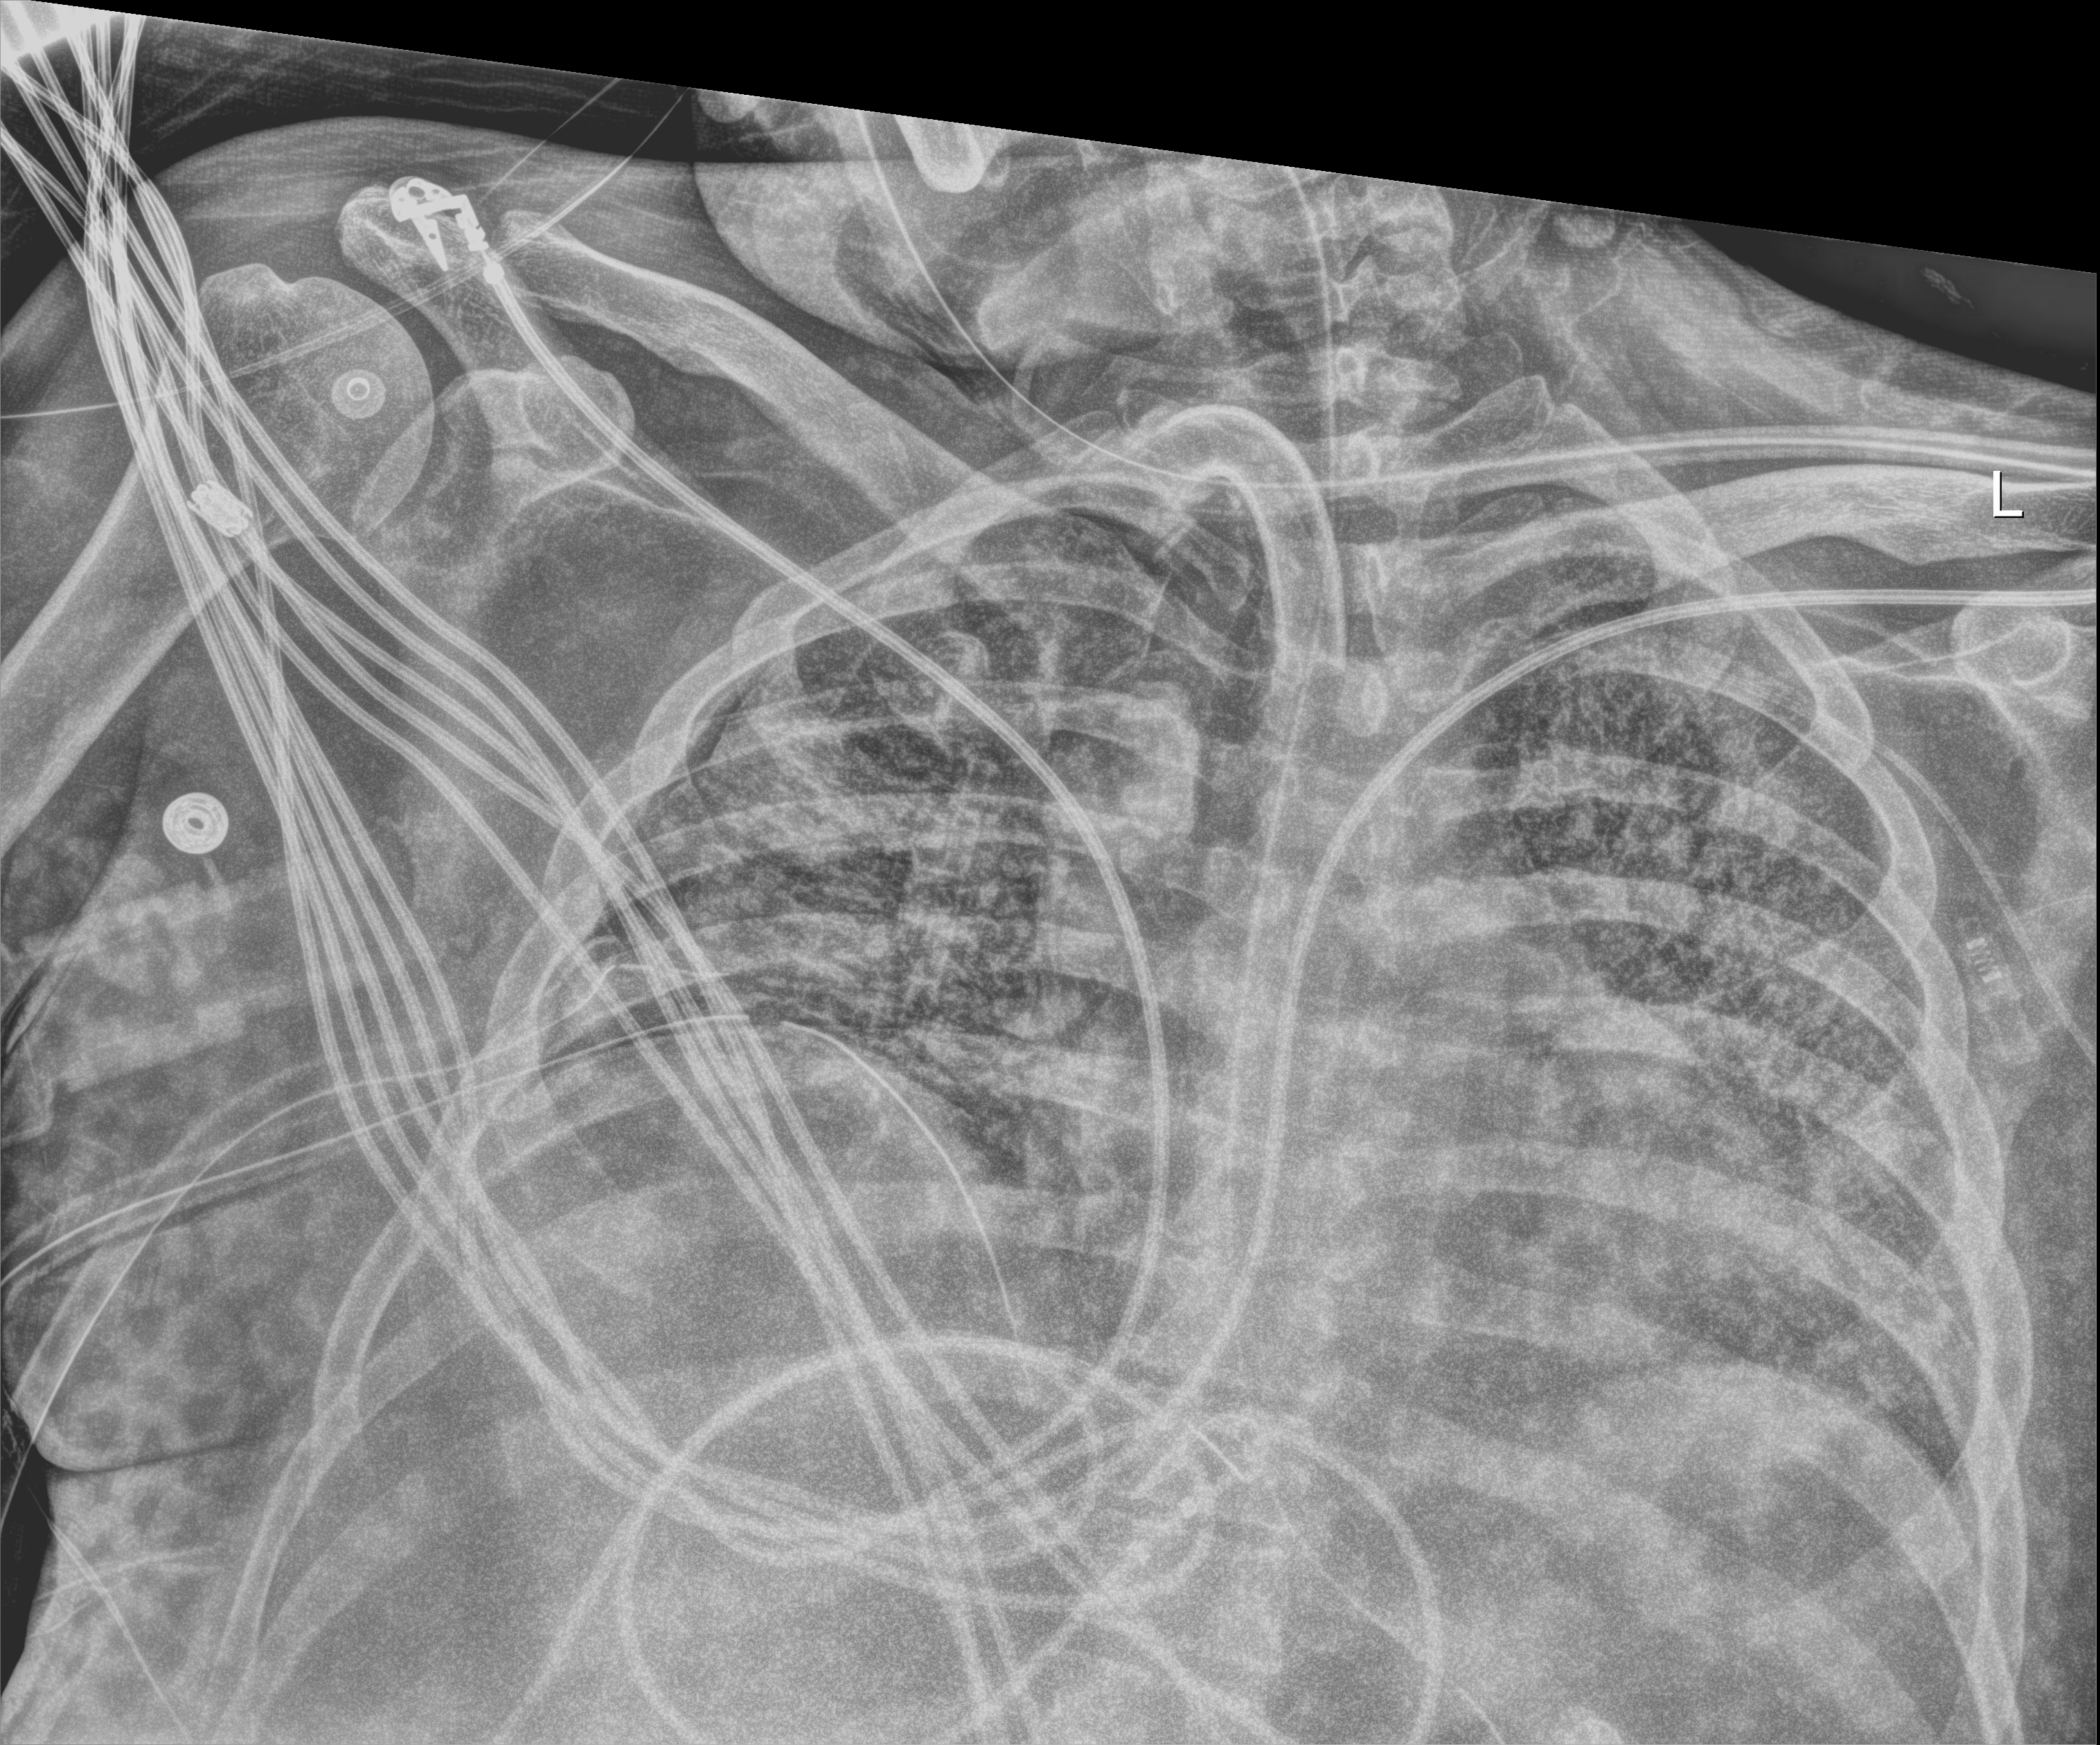
Chest radiograph (digital radiography), anteroposterior (AP) projection. Male patient hospitalised with COVID-19, age 18–59 years.
Hospital-stay facts (about this admission, not read from this image; timing relative to this image not recorded): smoking status (admission record): never.